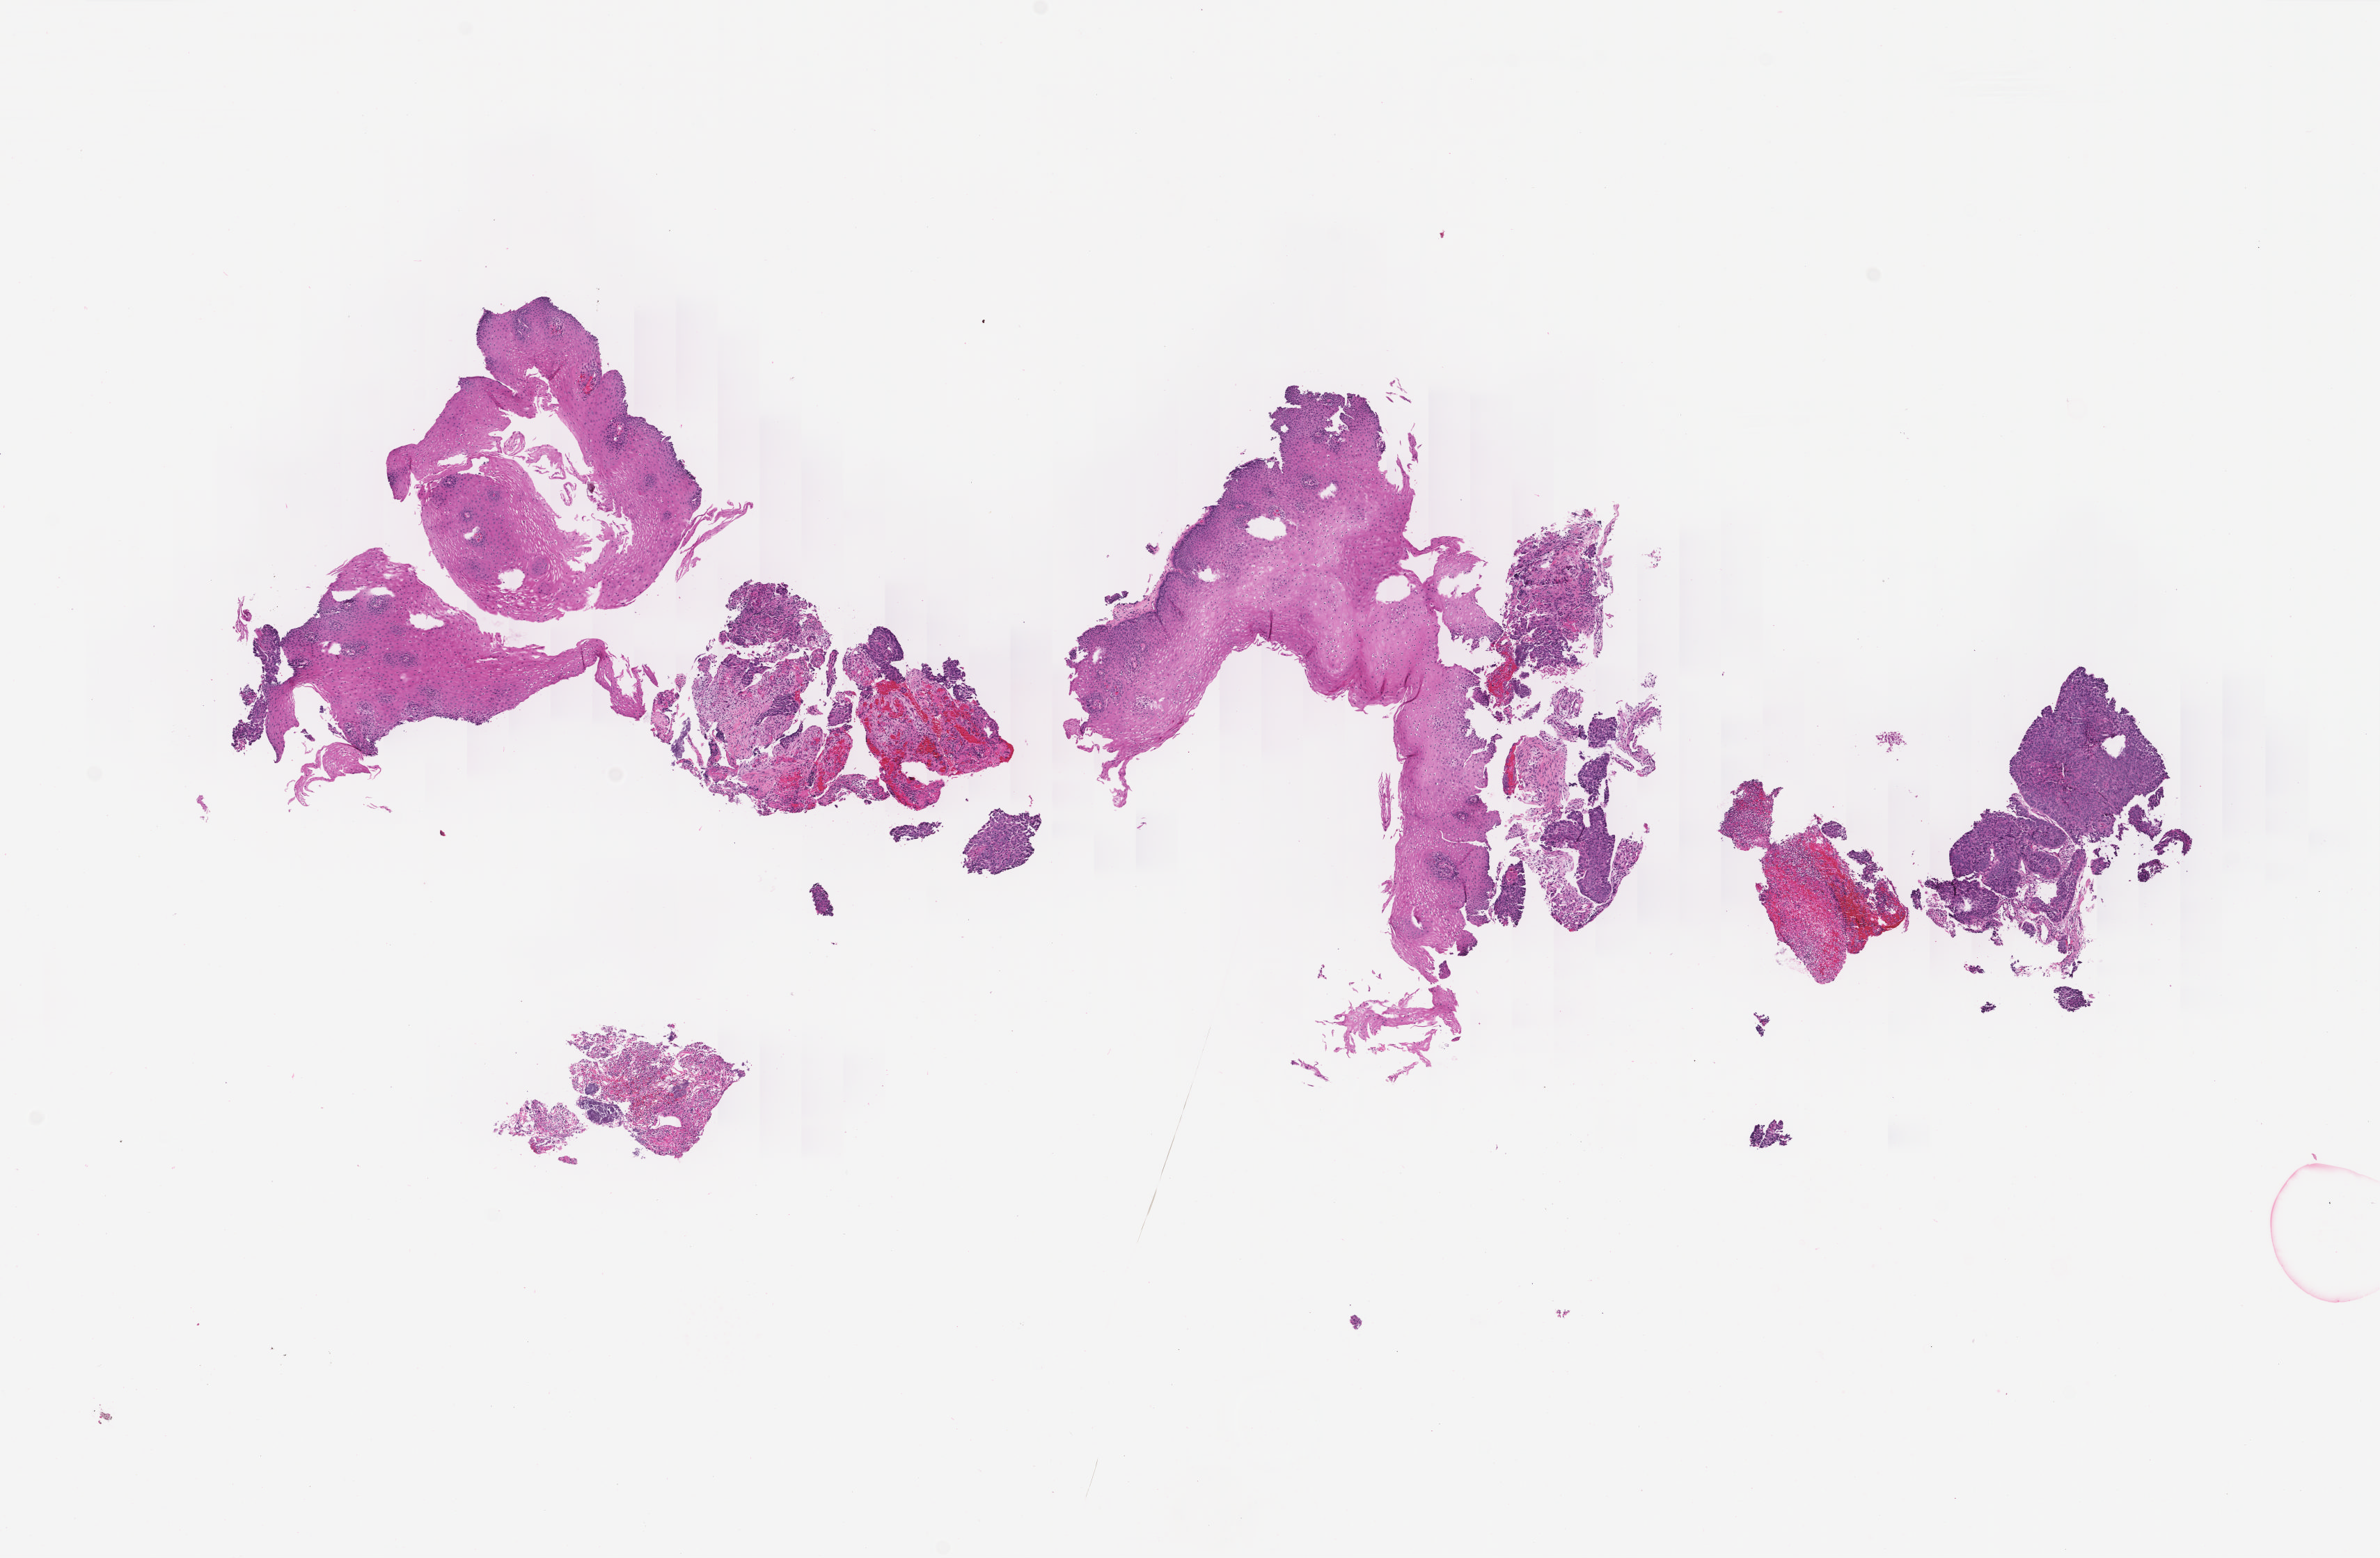
Digitized Hematoxylin and eosin (H&E) stained tissue section (whole slide) — low-resolution overview of the scanned area, about 13.7 x 9.0 mm, FFPE section, esophagus, primary tumour sample. Patient: male, age at initial diagnosis 55 years. Histologic grade: GX (grade cannot be assessed).
- diagnosis: Squamous cell carcinoma, NOS (middle third of esophagus)